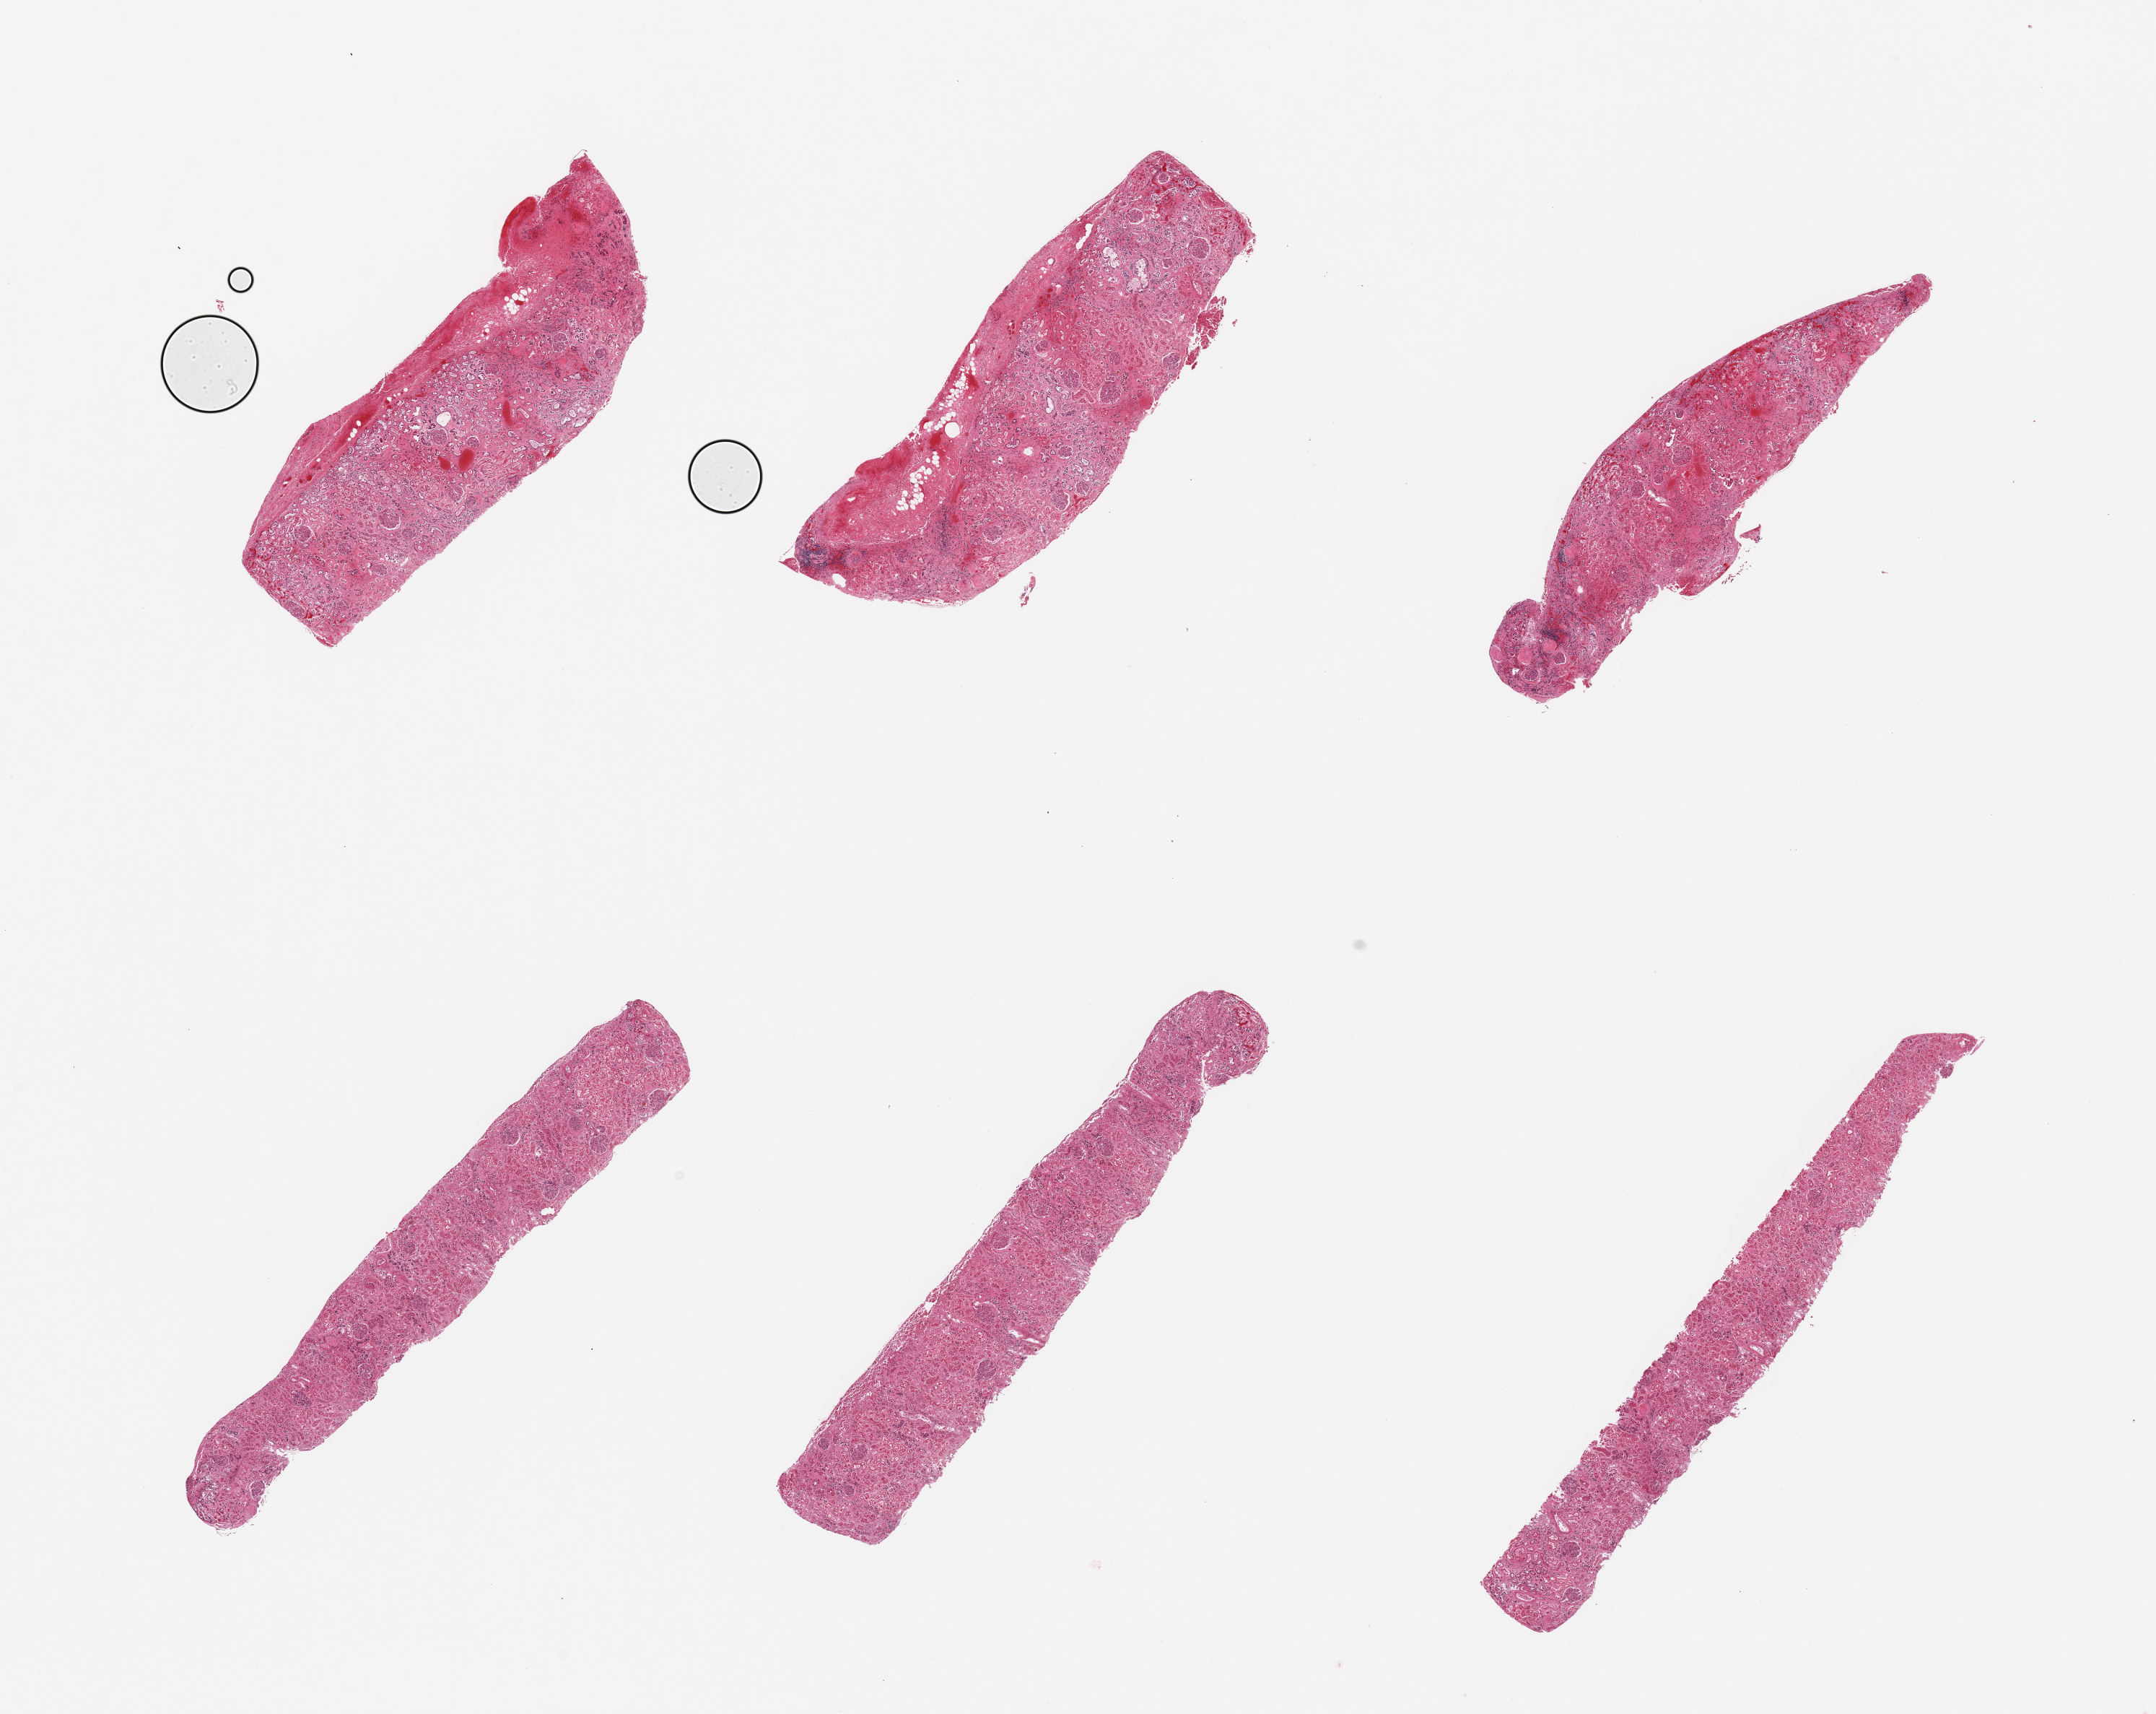
Whole-slide image, H&E stain, brightfield — whole scanned area (about 23.6 x 18.8 mm, acquisition: 20x scan) shown as a low-resolution overview, PAXgene-fixed, paraffin-embedded tissue, sampled site (target tissue): renal cortex, donor tissue sample.
Reviewer comment on this tissue sample: 6 pieces, glomeruli present, tubules badly autolyzed.